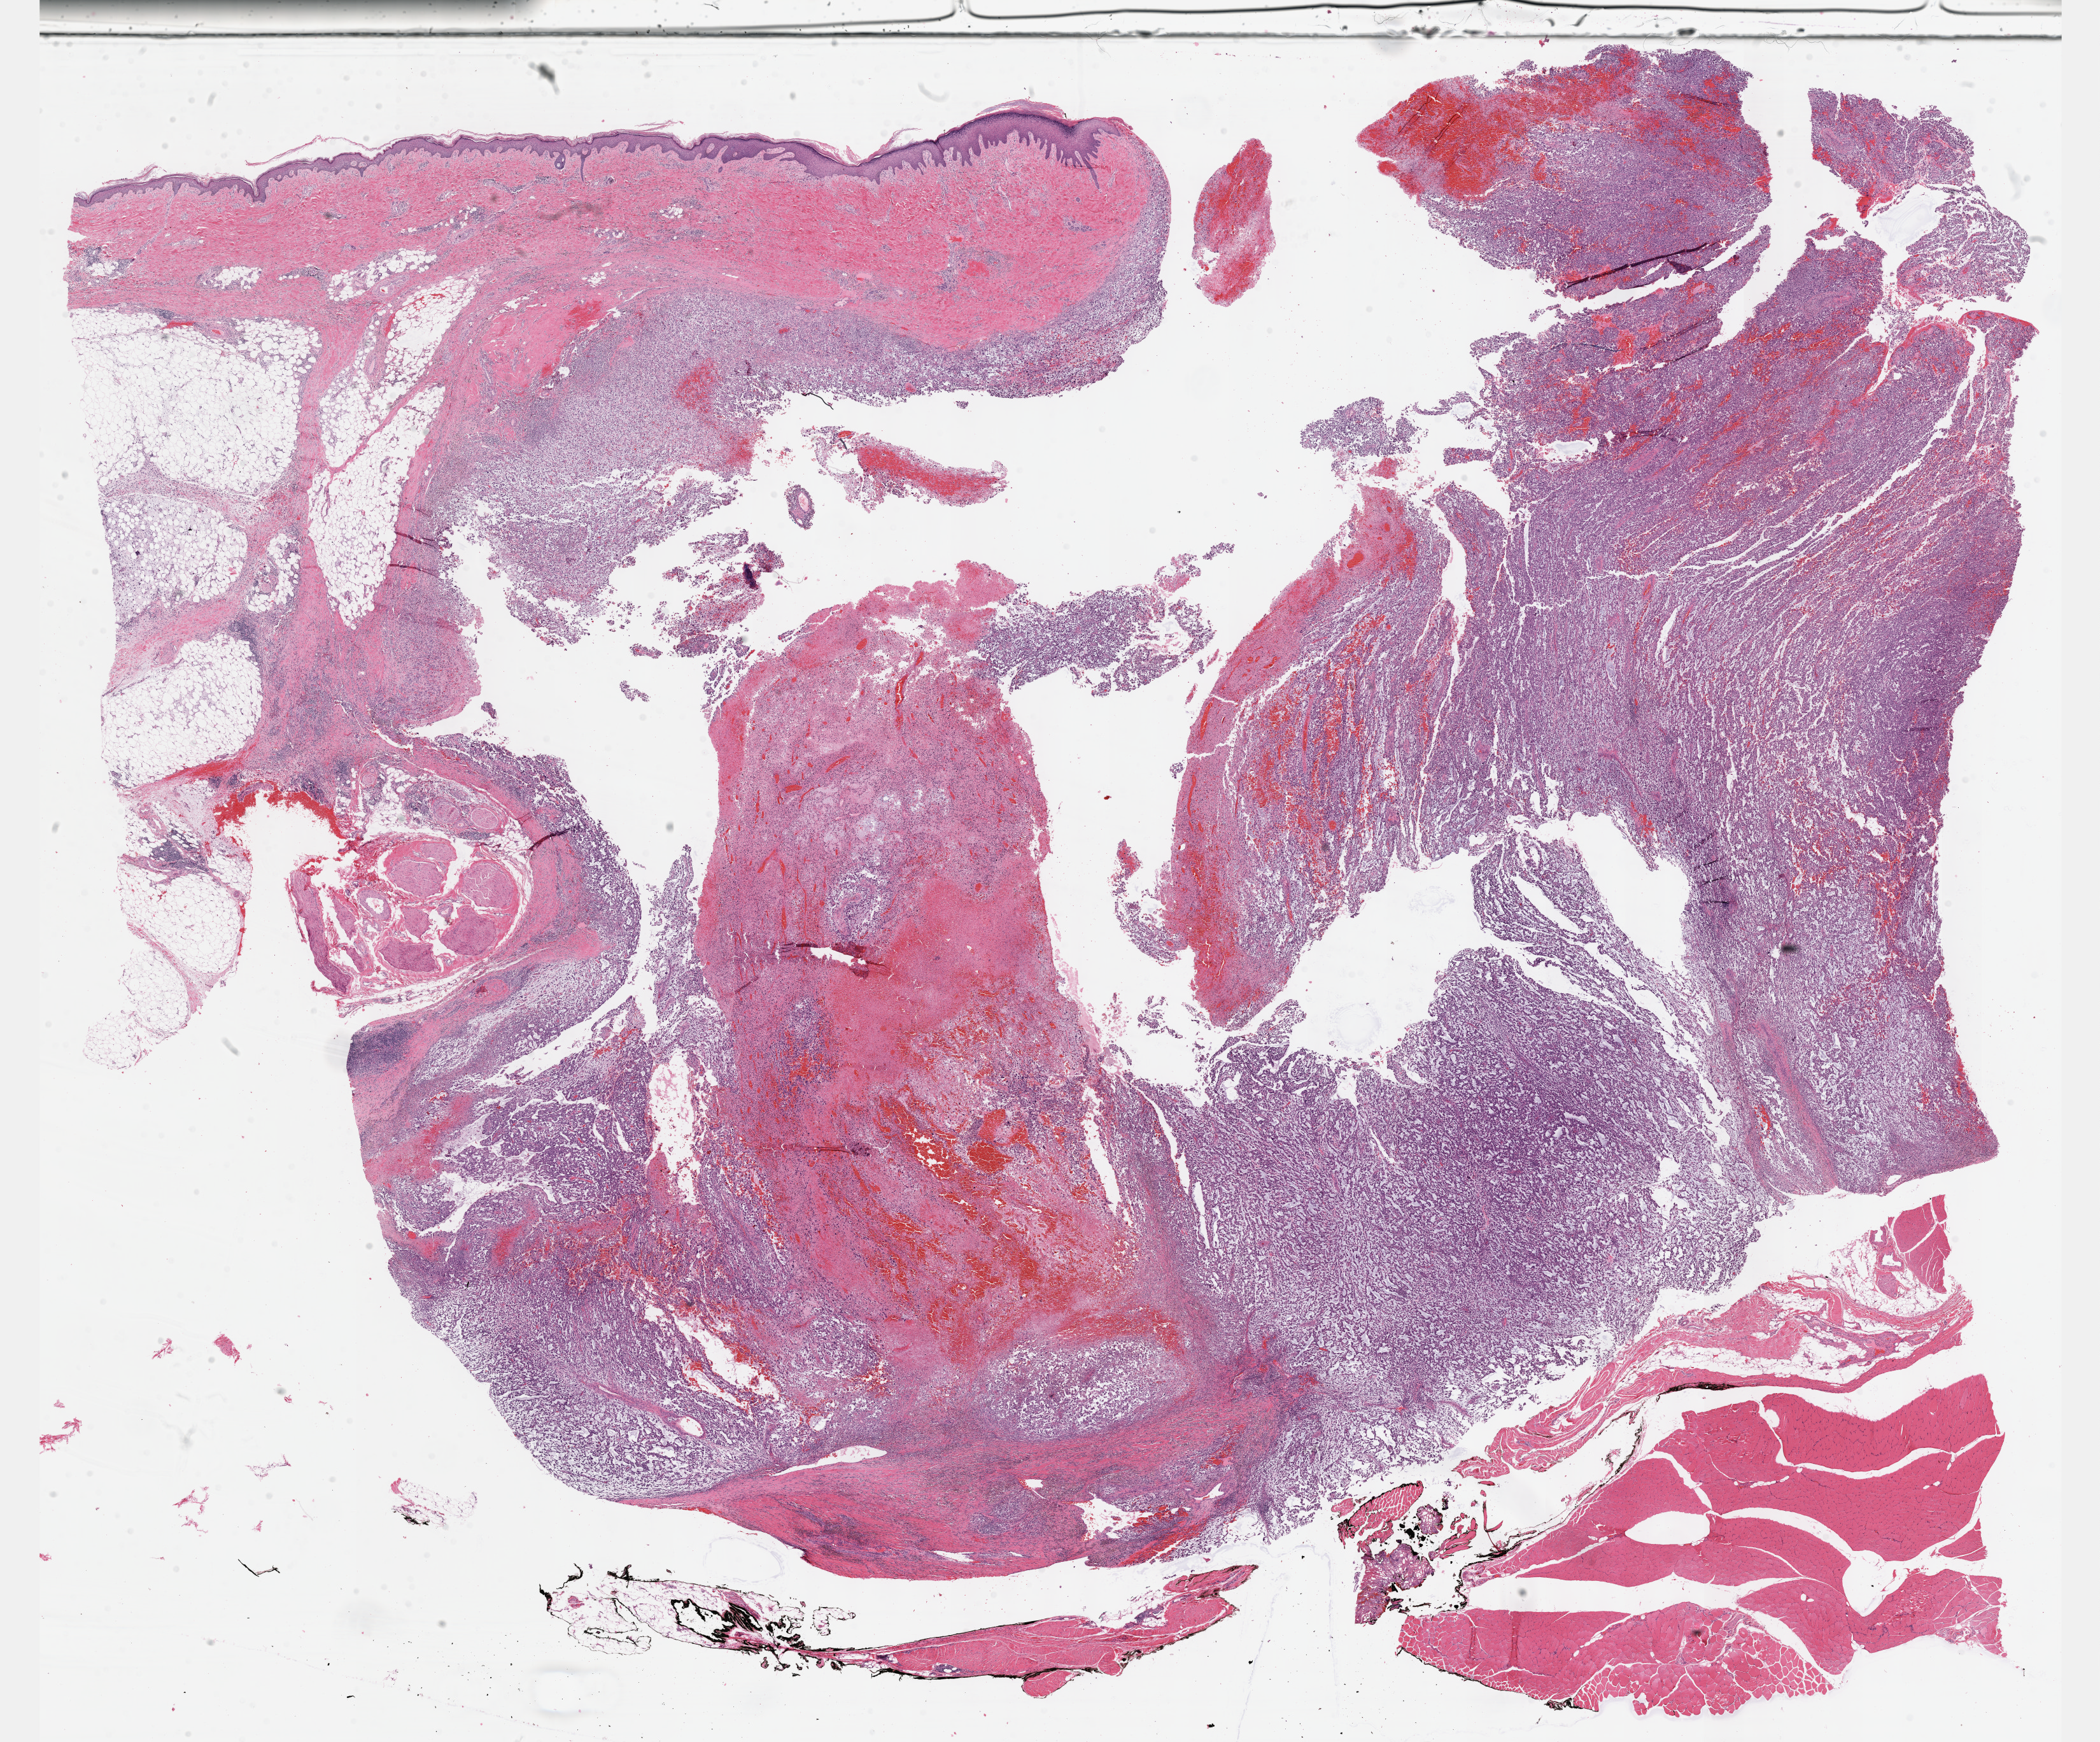
Digitized H&E-stained tissue section (whole slide) — low-resolution overview of the scanned area, about 26.7 x 22.1 mm (from a 40x scan). Formalin-fixed paraffin-embedded (FFPE) diagnostic section. Sample: primary tumour, connective, subcutaneous and other soft tissues. Female, age 59 years at initial diagnosis.
* pathologic diagnosis: Fibromyxosarcoma